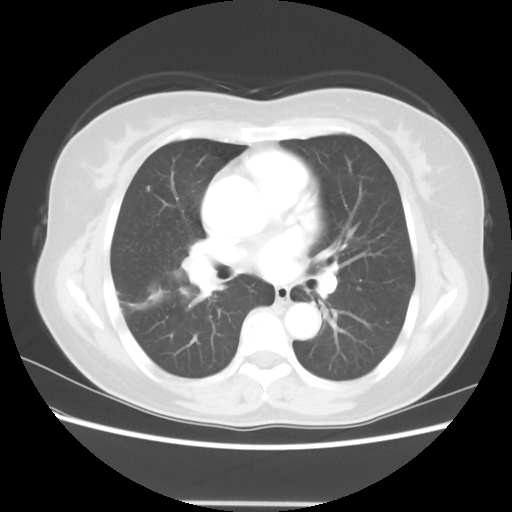
Chest CT, one axial slice; slice 32 of 56 in the series (ordered by position); reconstruction kernel STANDARD; 120 kVp; lung window (W 1500 / L -600 HU); 512 × 512 image matrix, field of view 360 × 360 mm. Patient: female, 55 years. From the clinical record (not read from this slice): clinical TNM (as recorded): T2 N1 M0.
Outlined on this slice (bounding box drawn by a radiologist):
- lung tumour (recorded histology: adenocarcinoma): bounding box <138,252,212,327> (left, top, right, bottom; pixels)